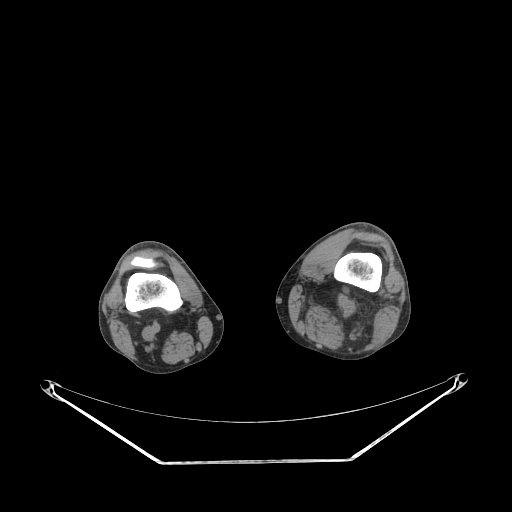
CT of an extremity soft-tissue mass (from a PET/CT study), one axial slice. Slice 197 of 267 in the series (ordered by position). Reconstruction kernel STANDARD. 140 kVp. Soft-tissue window (W 400 / L 40 HU). 512 × 512 image matrix, field of view 500 × 500 mm. Male patient. From the clinical record (not read from this slice): histological type: undifferentiated pleomorphic liposarcoma; grade: high; site of the primary tumour: left thigh.
Structures marked on this image (expert contour drawn on MRI and transferred to this co-registered scan by the dataset authors):
- gross tumour volume including surrounding oedema: box from (x=297, y=290) to (x=375, y=323) px